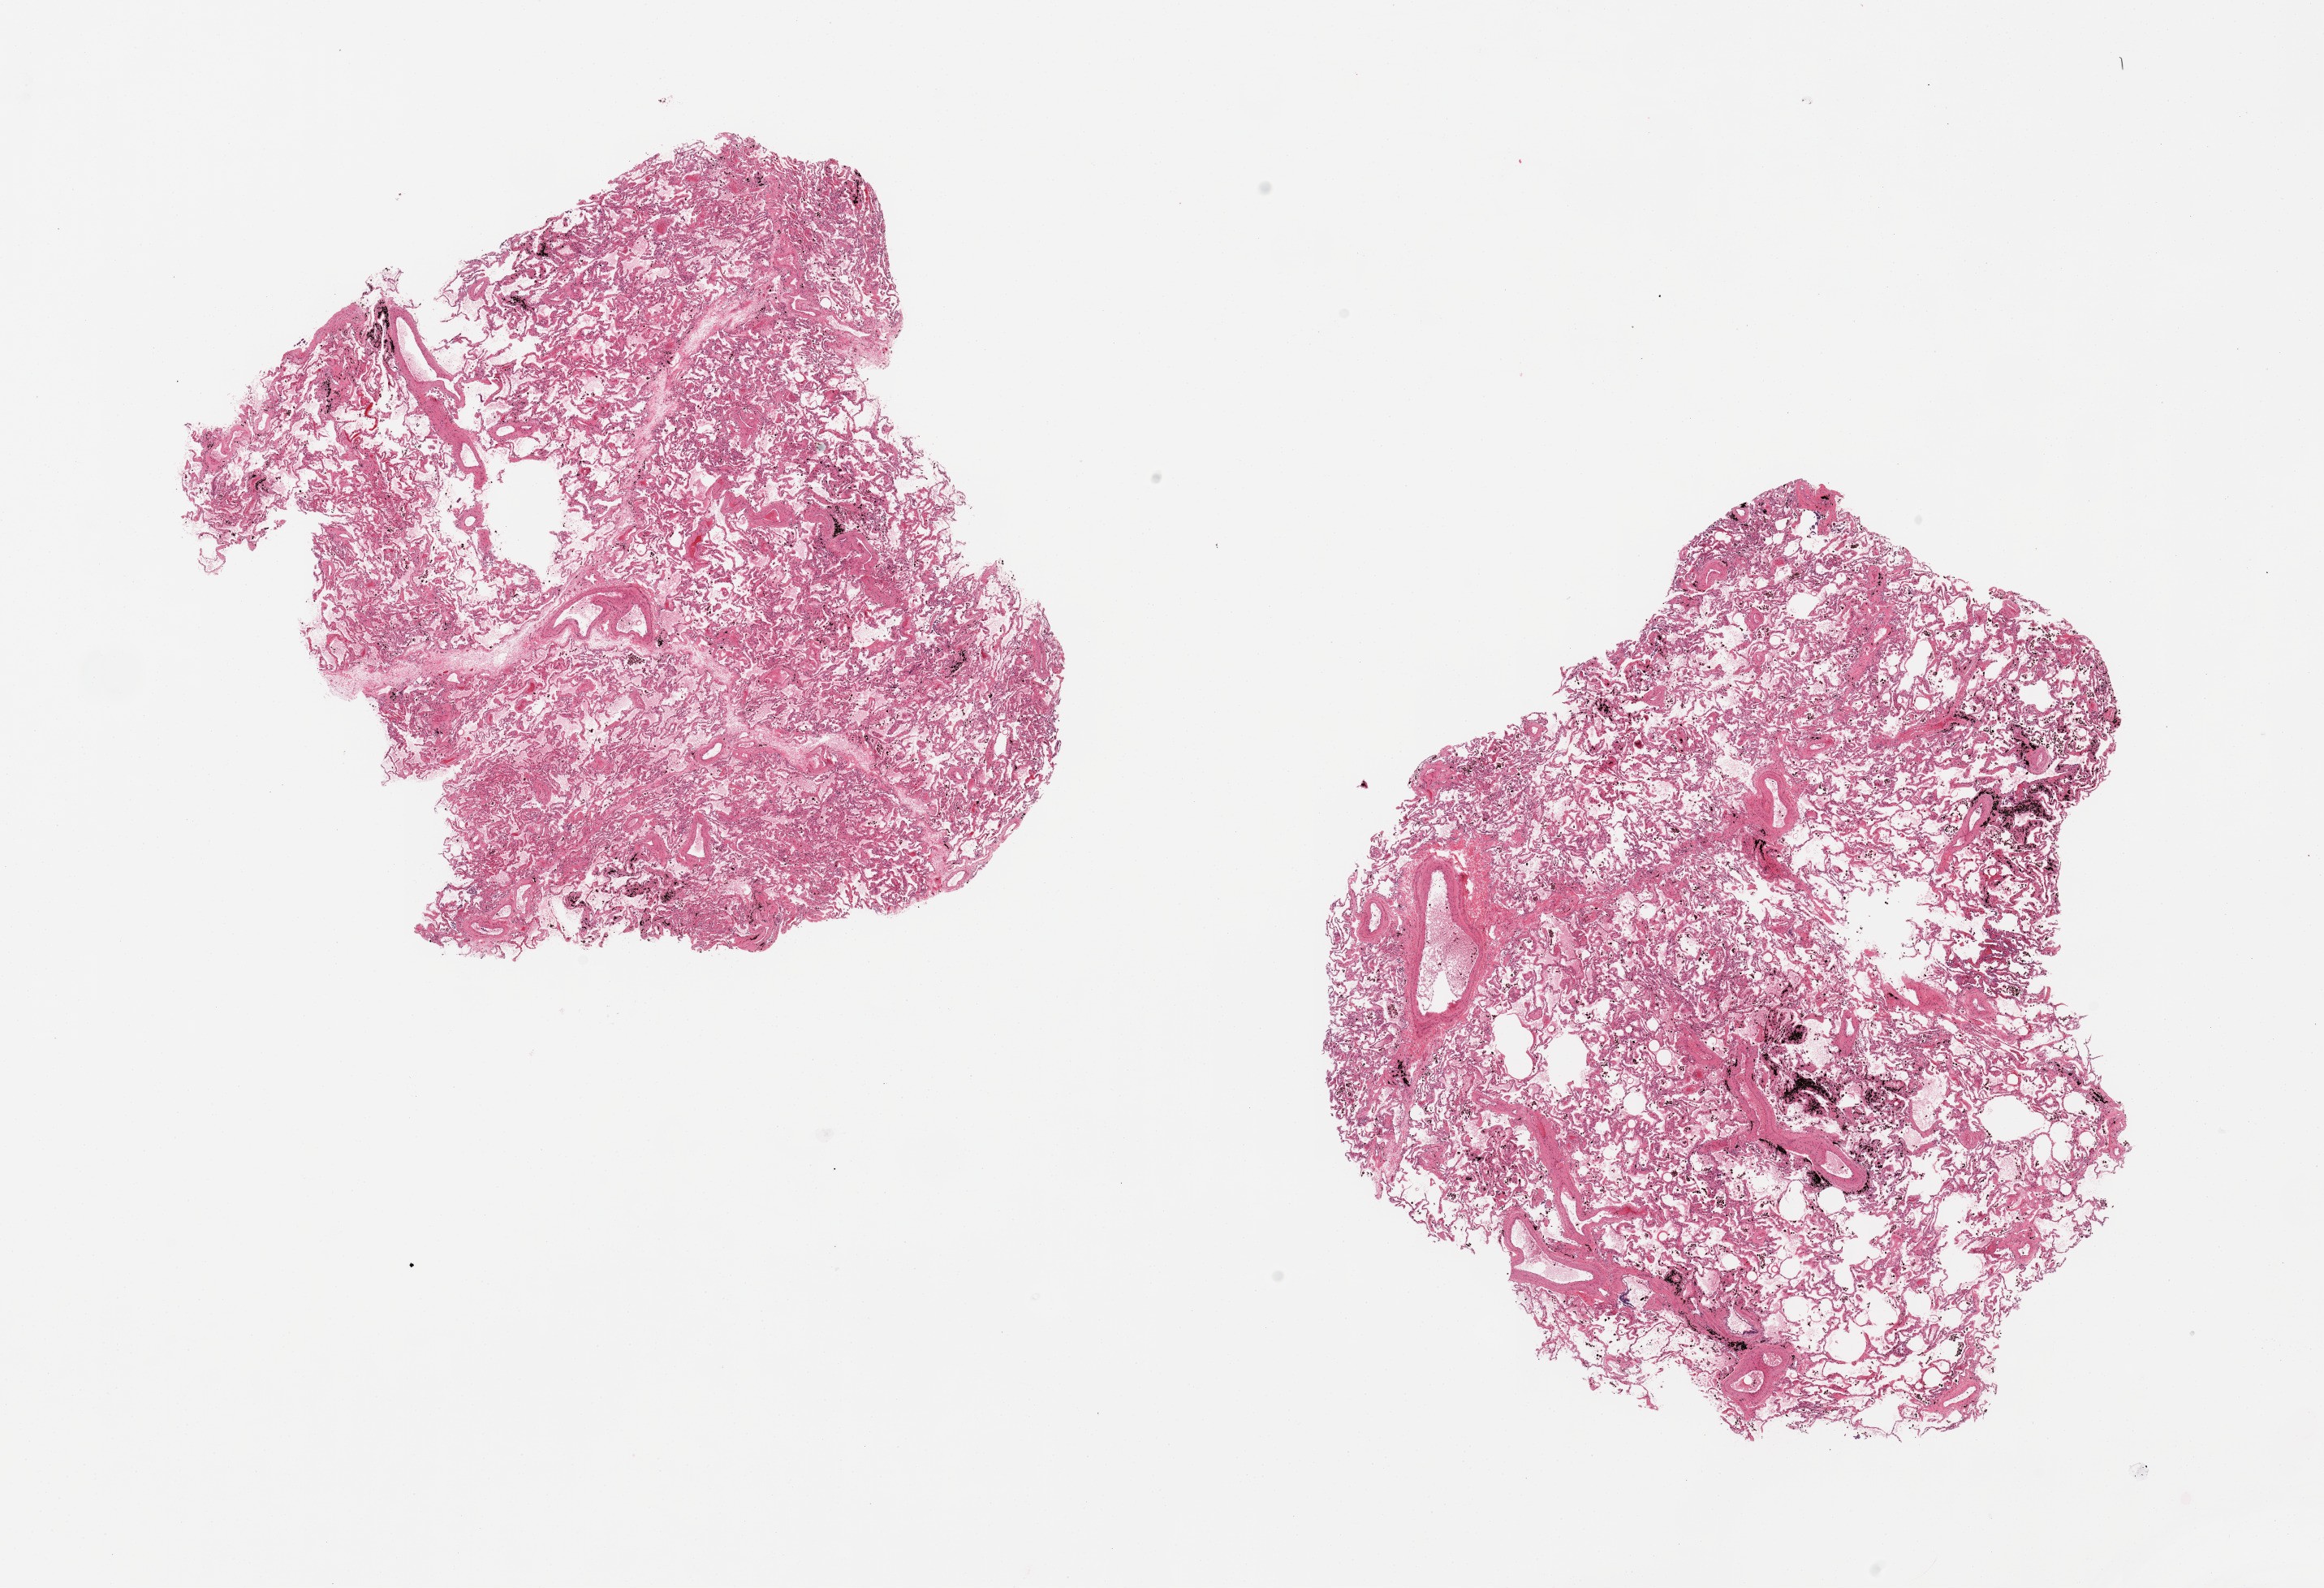
Haematoxylin and eosin whole-slide image, low-resolution overview of the scanned area, about 22.6 x 15.5 mm (from a 20x scan); PAXgene-fixed, paraffin-embedded tissue; target tissue: lung; tissue donor sample. Male donor.
Review note (as recorded): 2 pieces; hemosiderin-laden macrophages, anthracotic pigment, edema.